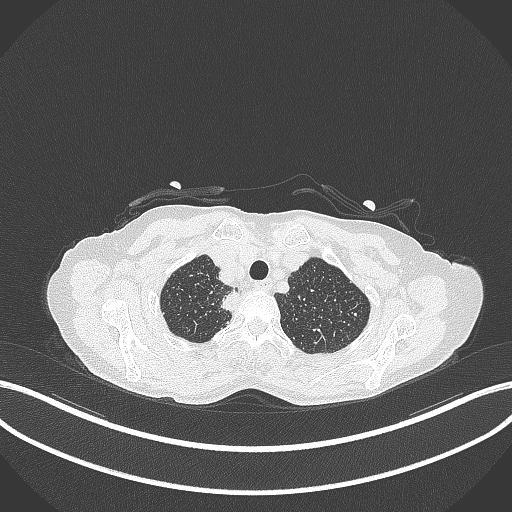
Chest CT, one axial slice; position 330 of 403 along the scan axis; reconstruction kernel B70f; lung window (W 1500 / L -600 HU); 1 mm slice thickness; 512 × 512 image matrix, field of view 400 × 400 mm. Female patient, age 75 years. From the clinical record (not read from this slice): clinical TNM (as recorded): T1c N1 M1.
Annotated regions visible in this slice (rectangle marked by the reading radiologist):
- lung tumour (recorded histology: adenocarcinoma): bounding box <219,288,244,314> (left, top, right, bottom; pixels)